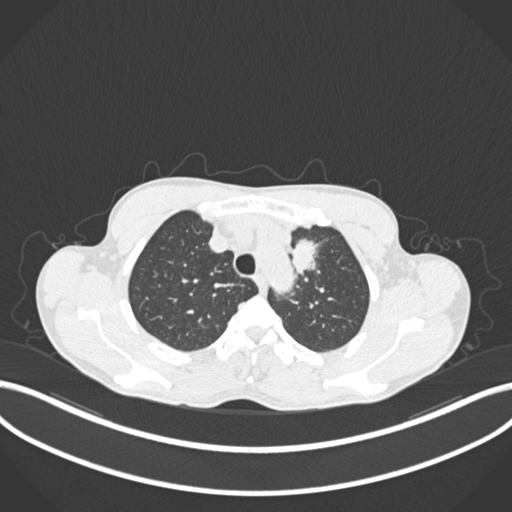
Chest CT, one axial slice. Slice 165 of 211 in the series (ordered by position). Reconstruction kernel B30f. Lung window (W 1500 / L -600 HU). 1 mm slice thickness. 512 × 512 image matrix, field of view 400 × 400 mm. Male patient, age 58 years. From the clinical record (not read from this slice): clinical TNM (as recorded): T1c N1 M0.
Annotated regions visible in this slice (bounding box drawn by a radiologist):
- lung tumour (recorded histology: adenocarcinoma): bounding box <282,238,324,283> (left, top, right, bottom; pixels)